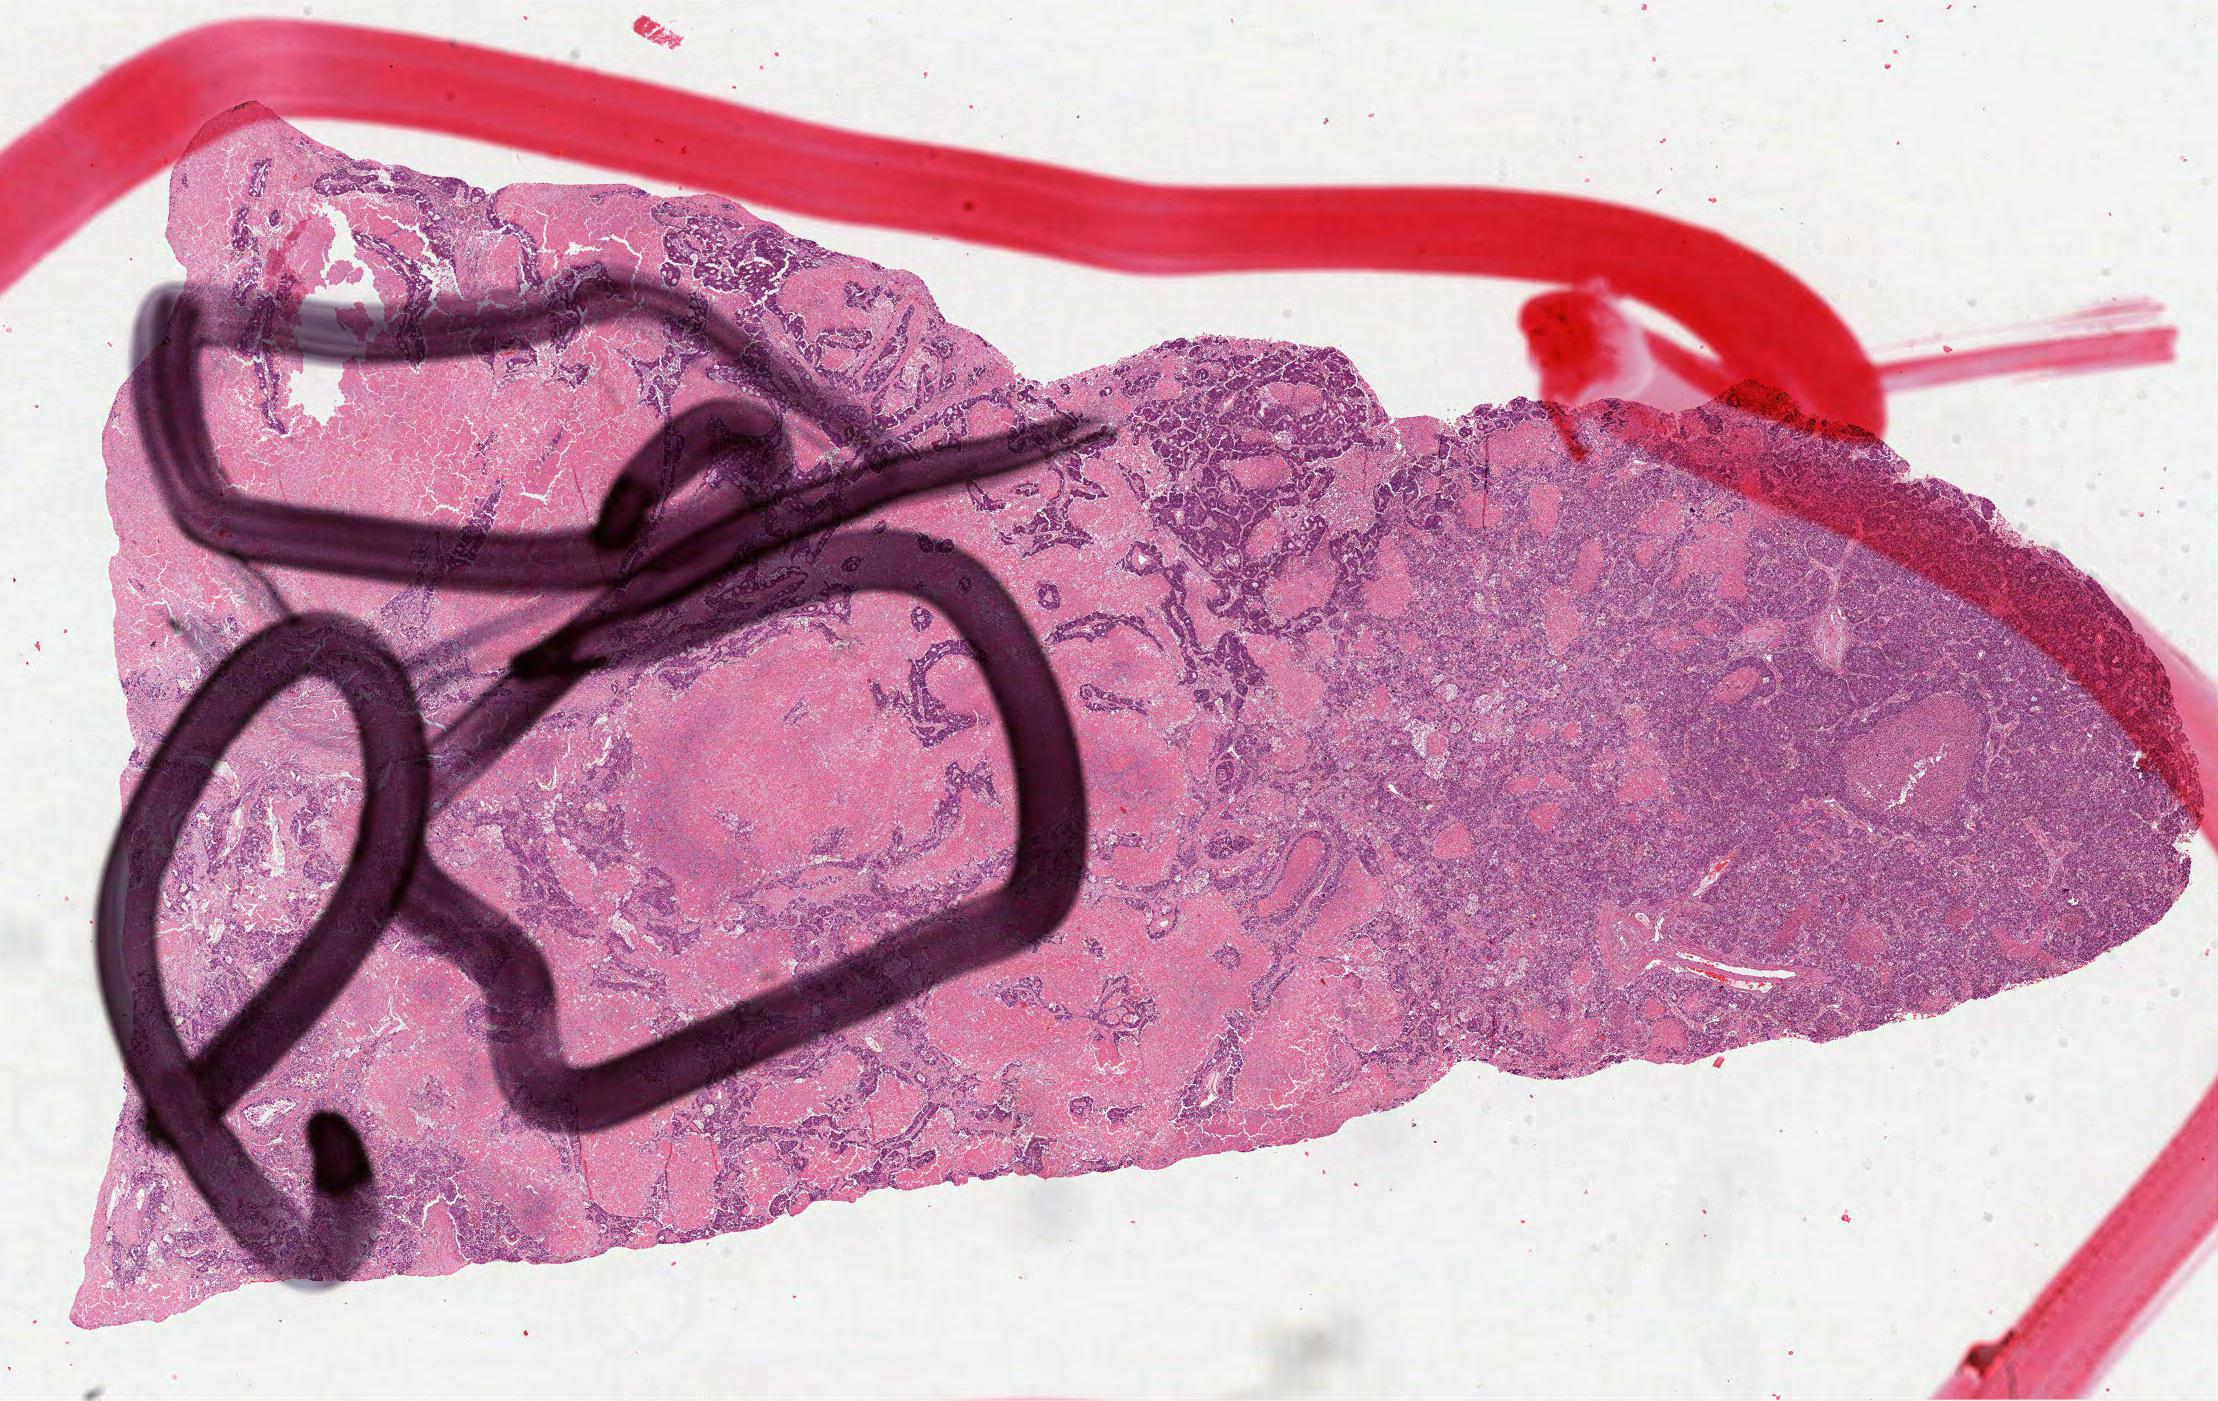
Digitized H&E tissue section (whole slide) — a low-resolution overview of the entire scanned area, about 17.9 x 11.3 mm, formalin-fixed paraffin-embedded (FFPE) diagnostic section, sample: primary tumour, lung. Male, age 61 years at initial diagnosis.
- AJCC pathologic stage: IIB
- pathologic diagnosis: Acinar cell carcinoma (upper lobe, lung)